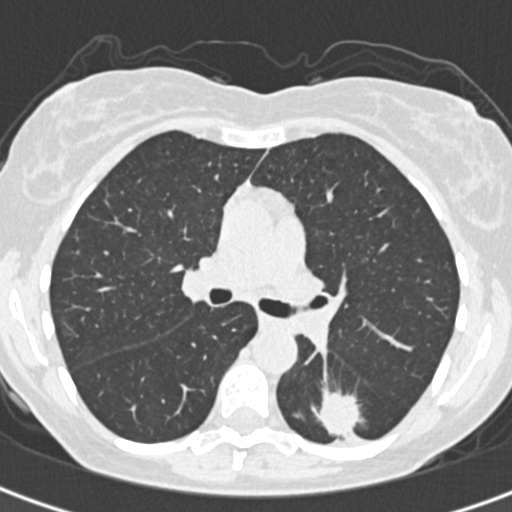
Low-dose screening chest CT, one axial slice. Slice 204 of 328 in the series (ordered by position). Reconstruction kernel B30f. 120 kVp. Lung window (W 1500 / L -600 HU). 1 mm slice thickness. 512 × 512 image matrix, field of view 284 × 284 mm.
Annotated regions visible in this slice (expert manual segmentation):
- lesion 1 (tumor, lower lobe of left lung): bounding box <315,390,361,436> (left, top, right, bottom; pixels)